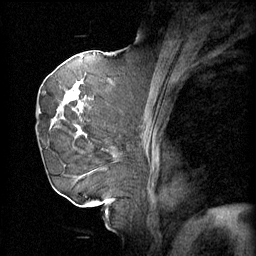
Breast MRI (dynamic contrast-enhanced), one sagittal slice; position 30 of 60 along the scan axis; 4 images stored at this slice position (order not interpretable as contrast timing); 1.5 T; TE 4.2 ms, TR 11 ms; 256 × 256 image matrix. Female patient, age 72 years.
Structures marked on this image (semi-automatic segmentation, software-assisted and operator-edited):
- analysis volume of interest (the breast-tissue region the enhancement analysis was run in; not a lesion): bounding box (x1, y1, x2, y2) in pixels: (43, 68, 109, 163)
- tumour enhancement mask (voxels above the 70 % enhancement threshold inside the analysis volume of interest): (44, 76, 96, 151)